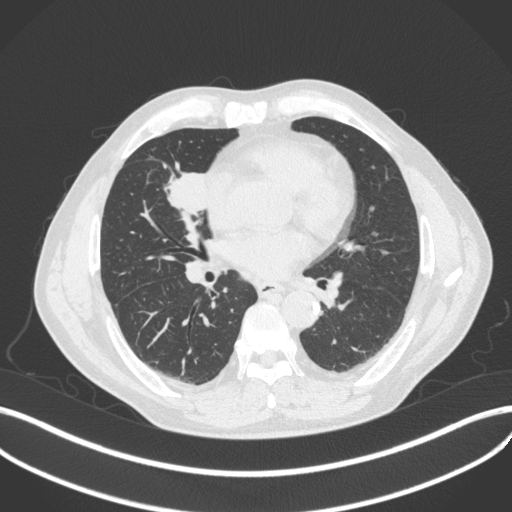
Chest CT, one axial slice. Position 191 of 429 along the scan axis. 120 kVp. Lung window (W 1500 / L -600 HU). 512 × 512 image matrix, field of view 400 × 400 mm. Patient: male, 61 years. Case-level facts recorded for this patient, not image findings: clinical TNM (as recorded): T2b N1 M0.
Structures marked on this image (bounding box drawn by a radiologist):
- lung tumour (recorded histology: squamous cell carcinoma): bounding box [x1, y1, x2, y2] px = [161, 161, 215, 218]